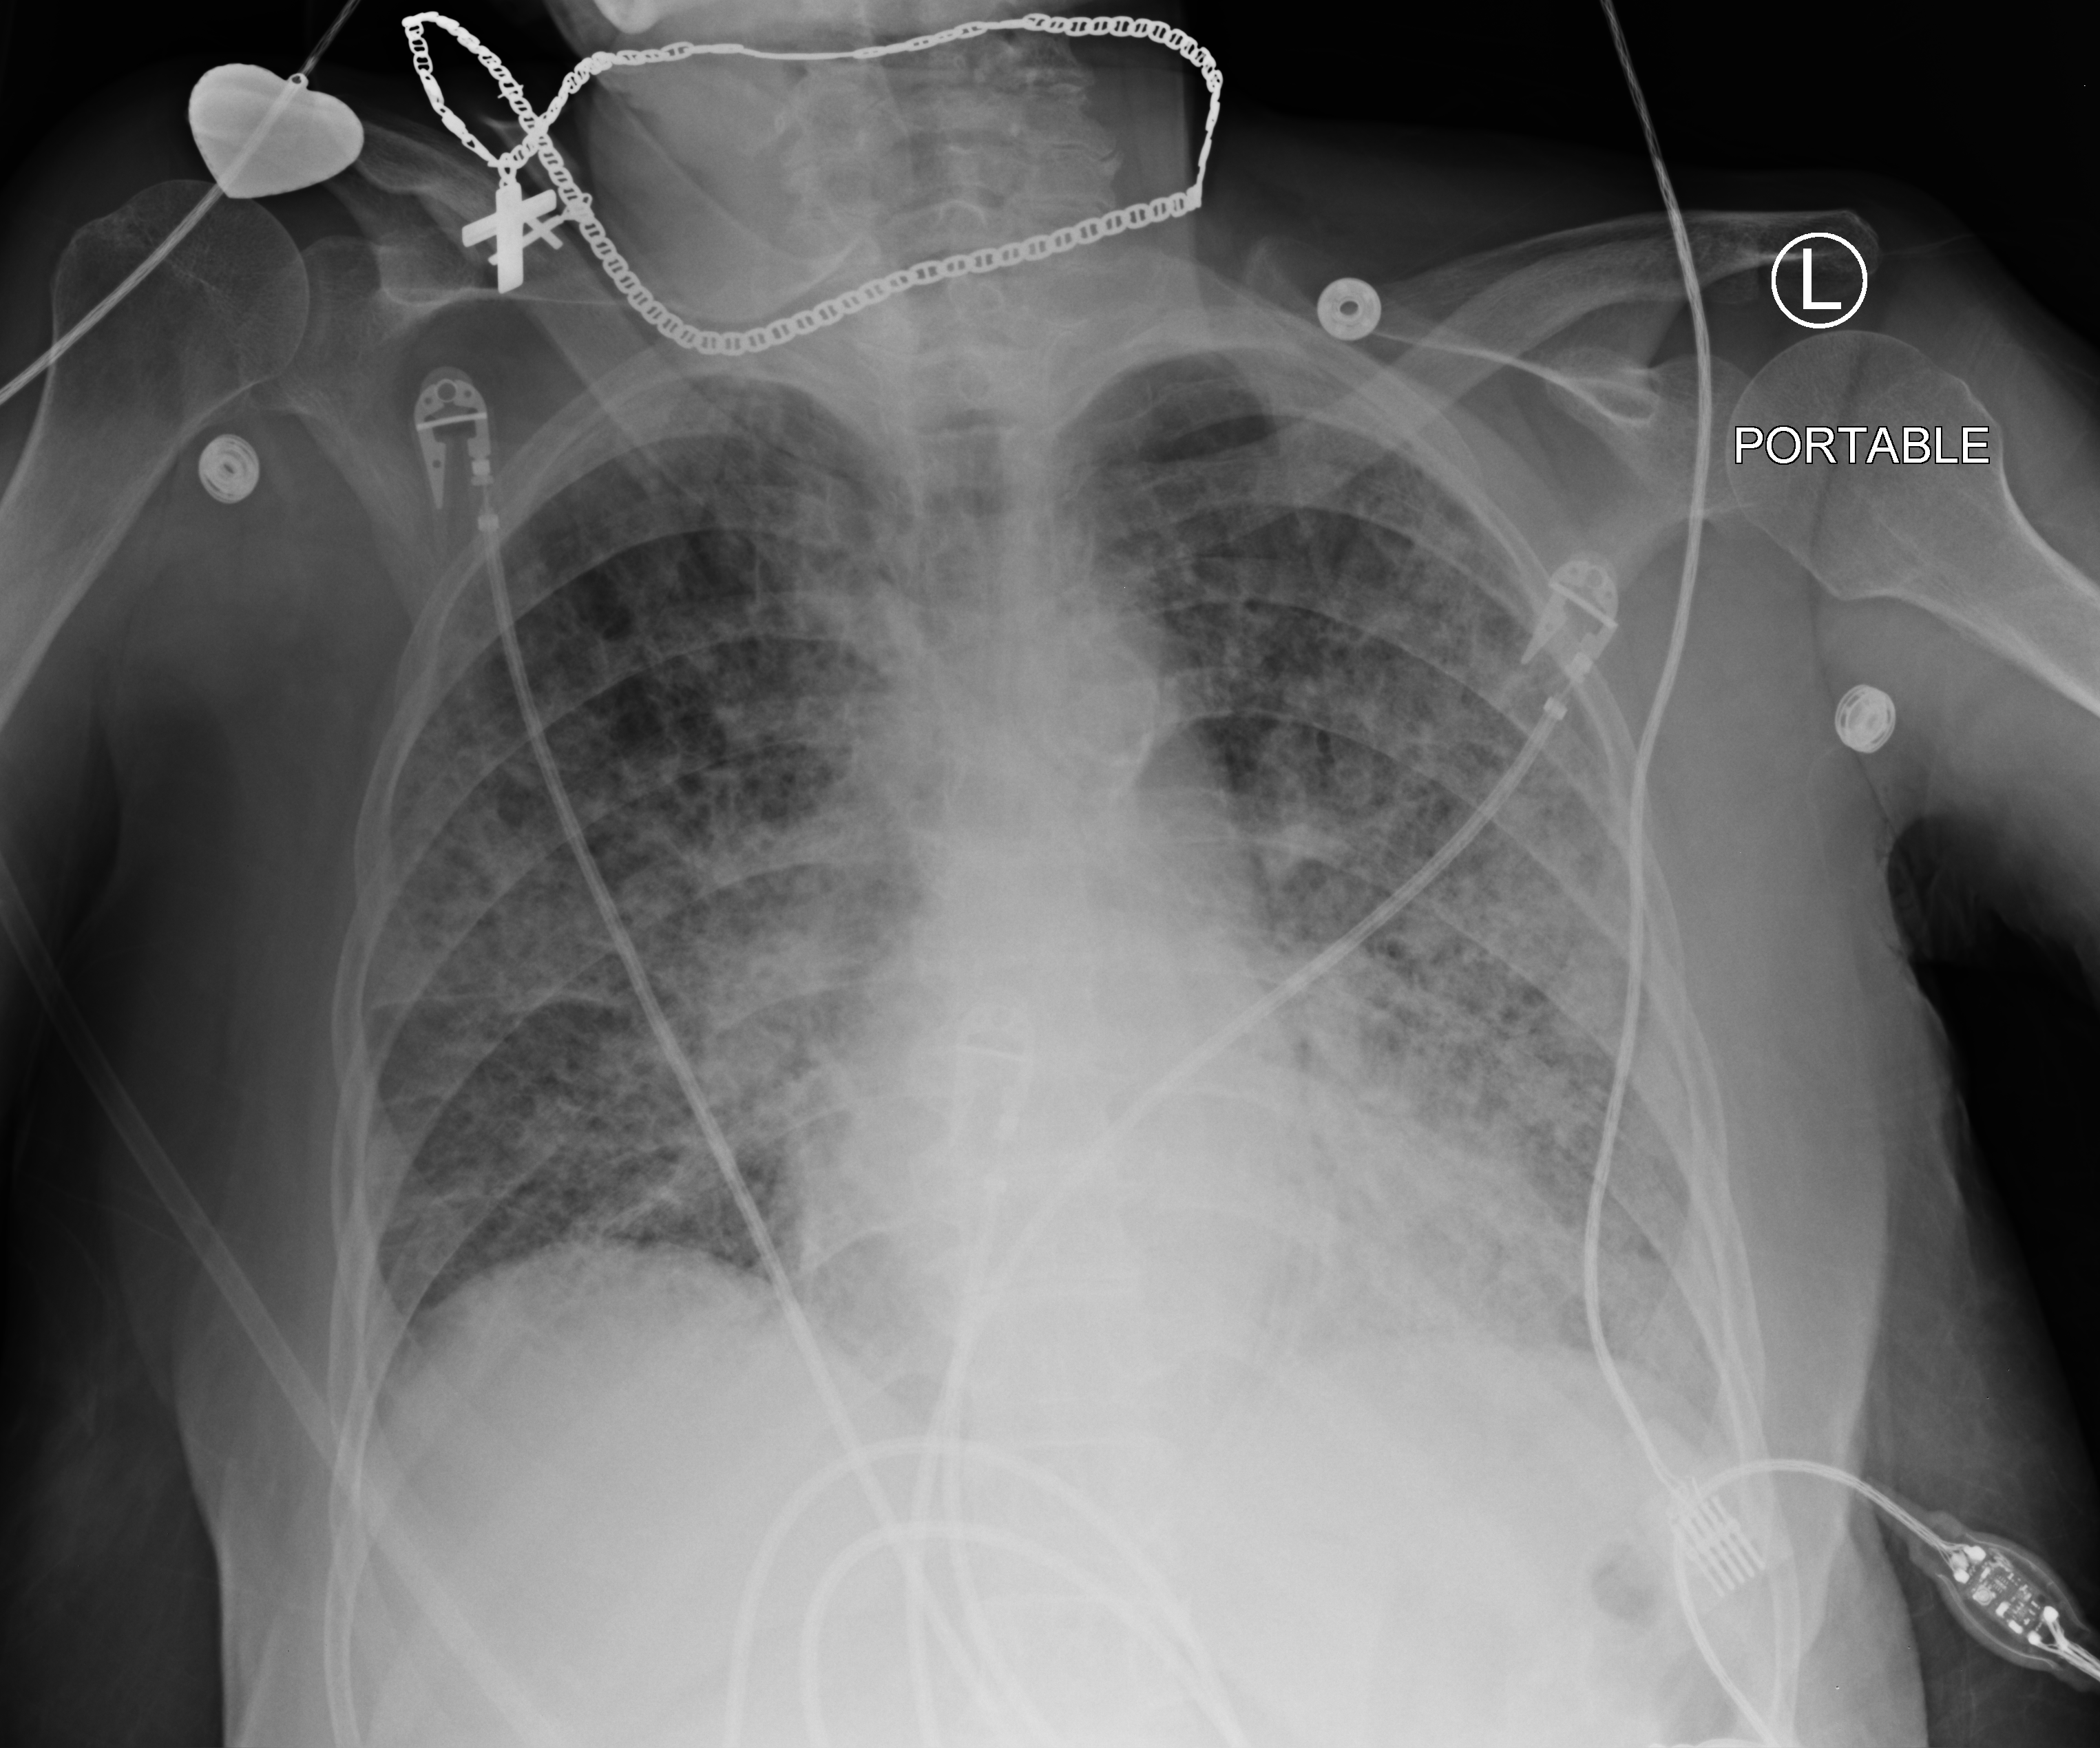
Bedside chest radiograph (computed radiography). Female patient hospitalised with COVID-19, age 75–90 years.
Hospital-stay facts (about this admission, not read from this image; timing relative to this image not recorded): smoking status (admission record): never; length of hospital stay: 13 days; admitted to intensive care during this hospital stay: no.